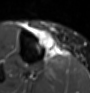
MRI of an extremity soft-tissue mass, one axial slice. STIR. MR volume resampled by the dataset authors to the PET/CT grid (not the native acquisition matrix). 90 × 93 image matrix. Female patient. Case-level facts recorded for this patient, not image findings: histological type: undifferentiated – high grade; grade: high; site of the primary tumour: right thigh.
Annotated regions visible in this slice (expert contour drawn on MRI and transferred to this co-registered scan by the dataset authors):
- gross tumour volume (mass): box from (x=35, y=28) to (x=59, y=59) px